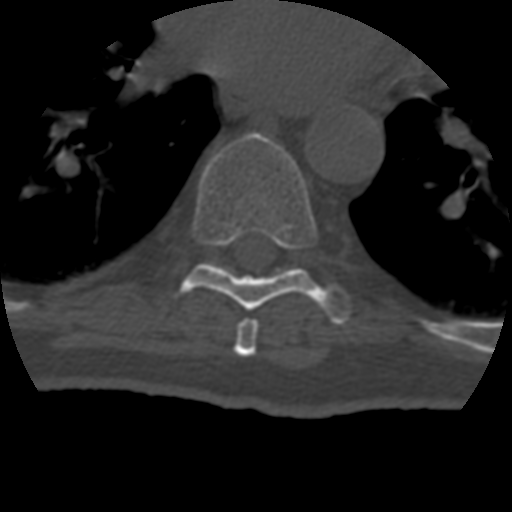
CT including the spine, one axial slice. Slice 258 of 399 in the series (ordered by position). Bone window (W 1800 / L 400 HU). 1.25 mm slice thickness. 512 × 512 image matrix. Patient age 69 years. From the clinical record (not read from this slice): primary cancer: prostate.
Outlined on this slice (semi-automatic segmentation, software-assisted and operator-edited):
- T7 vertebra: box from (x=234, y=319) to (x=259, y=357) px
- T8 vertebra: (x=160, y=132)–(x=351, y=324)